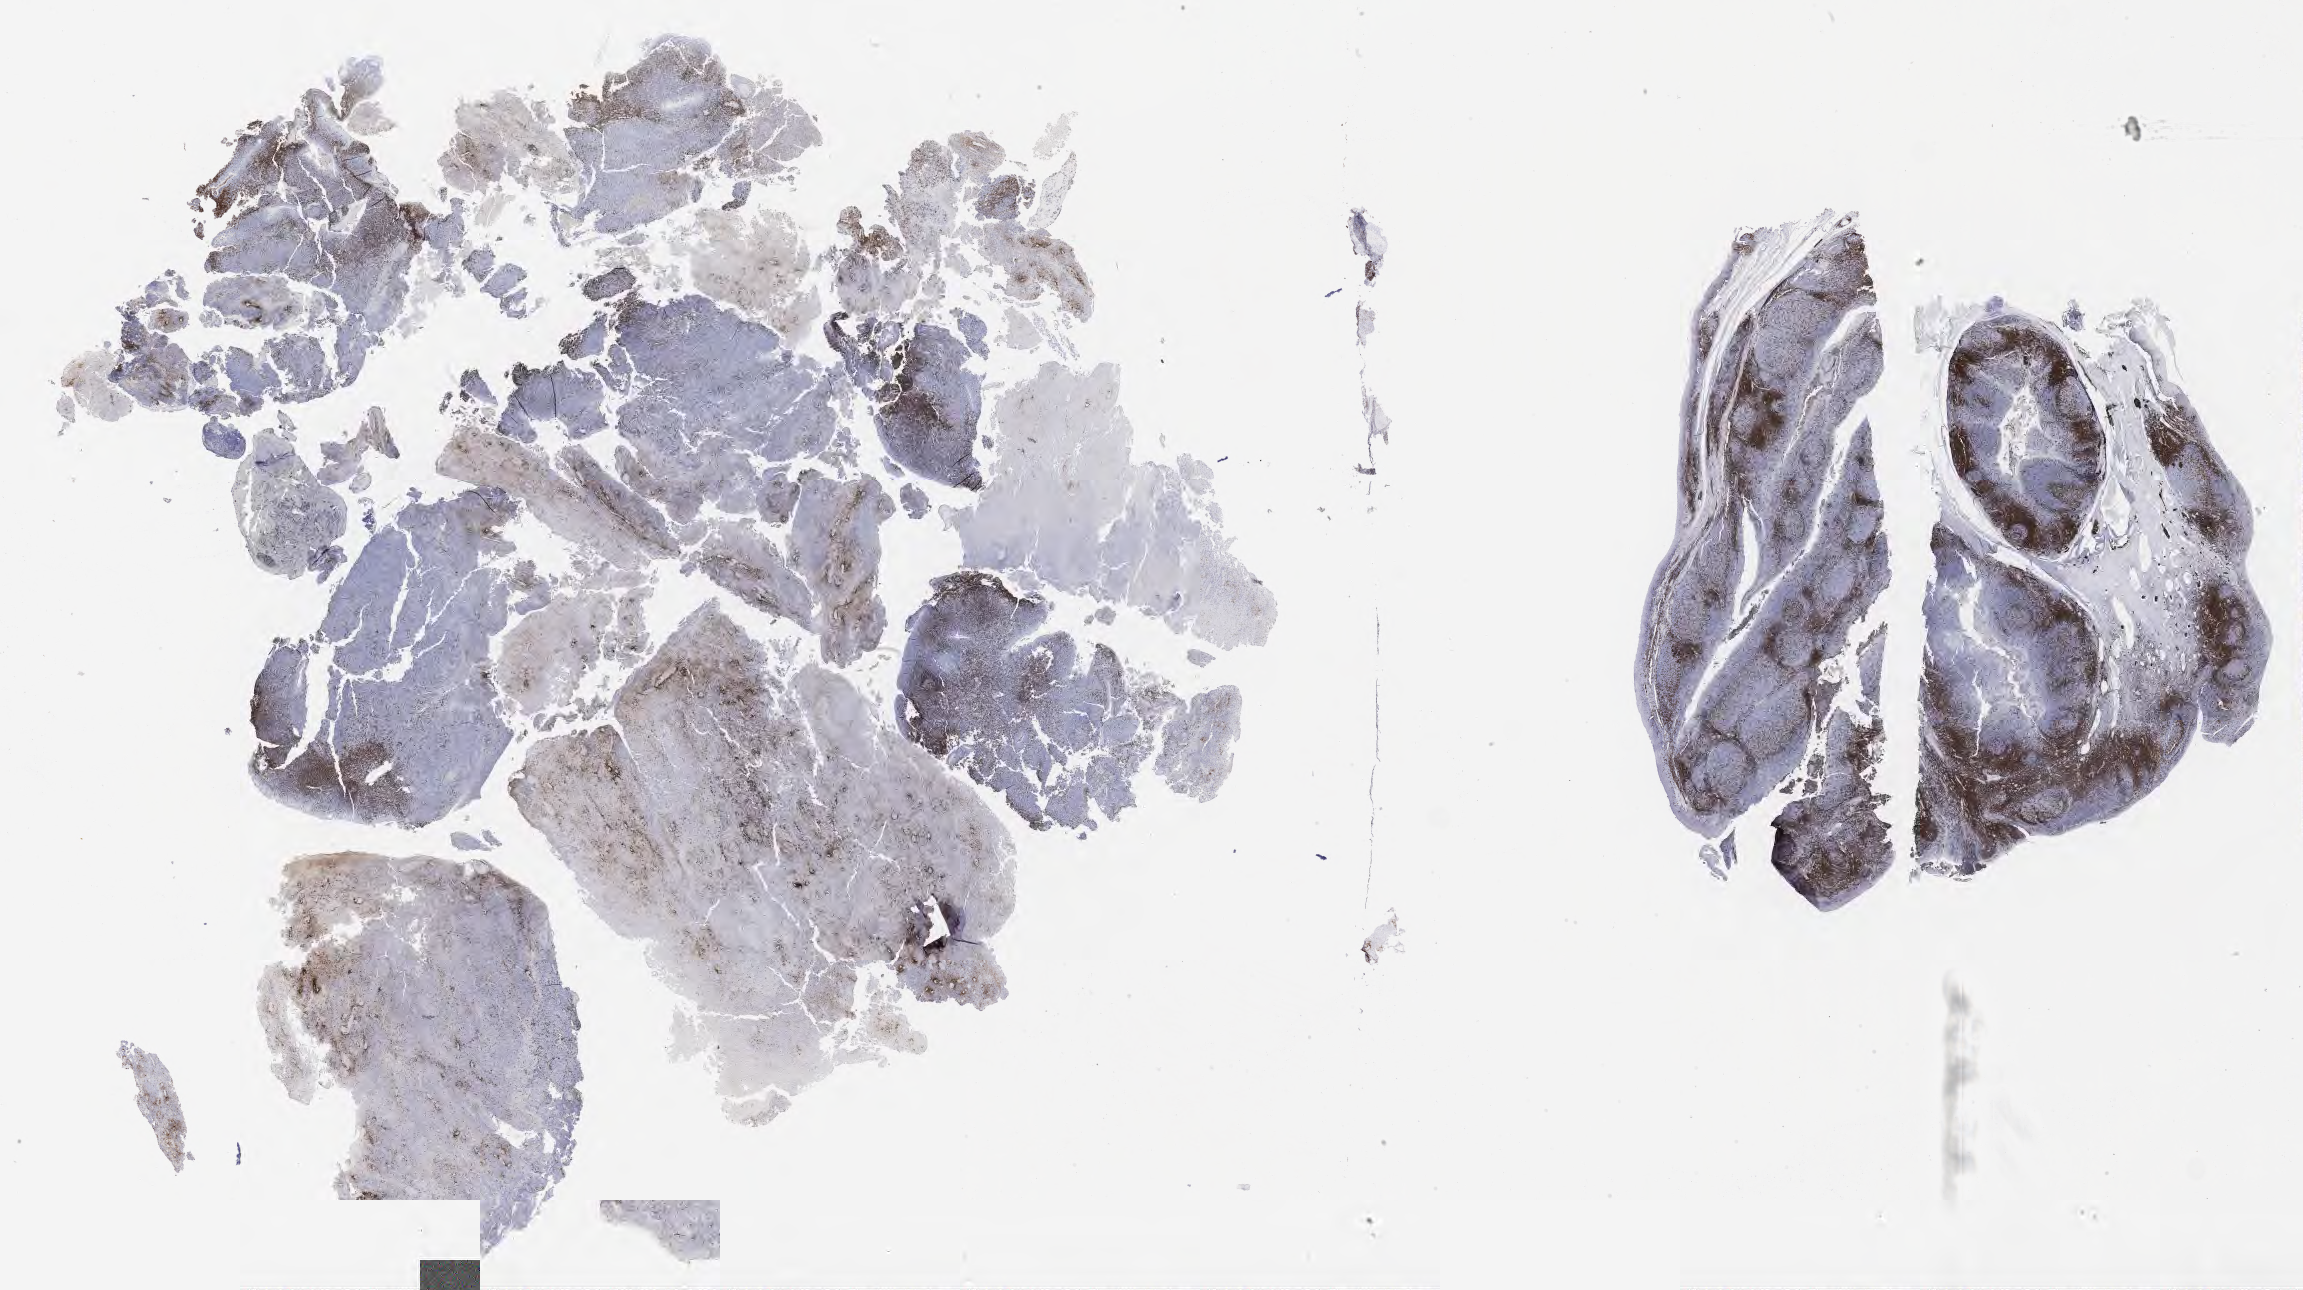
Immunohistochemistry (IHC) whole-slide image stained for CD3, whole scanned area (about 37.2 x 20.9 mm) shown as a low-resolution overview; tumor tissue. Male patient, 47 years old.
Diagnosis: Diffuse large B-cell lymphoma, NOS.